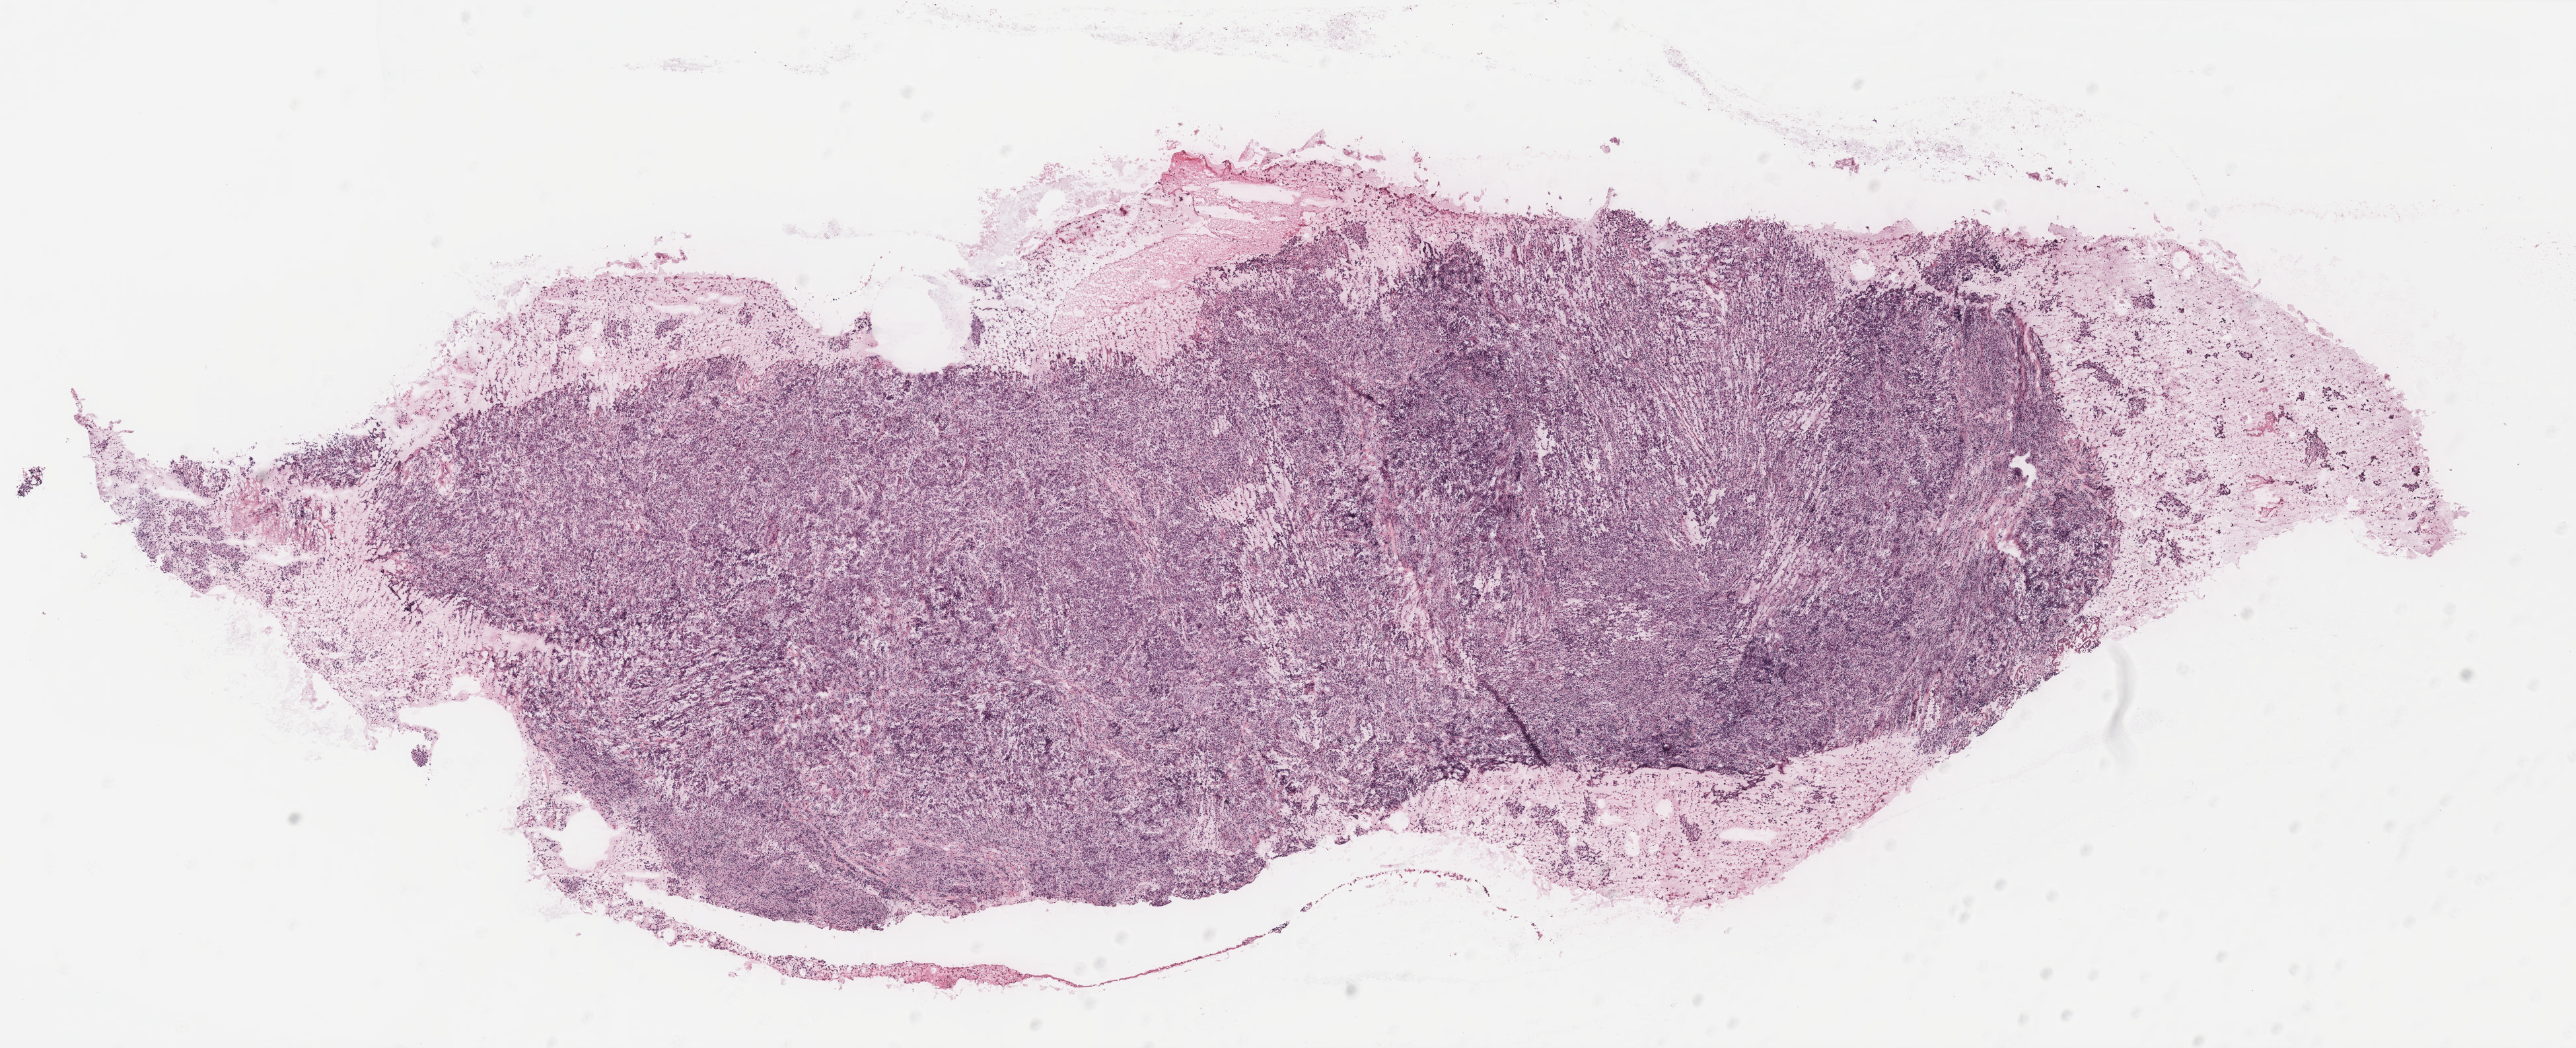
Whole-slide histology image, Hematoxylin and eosin (H&E) stained — low-resolution overview of the scanned area, about 15.6 x 6.4 mm (acquisition: 40x scan). Patient: female, age 48 years.
- specimen: tumour tissue sample, breast